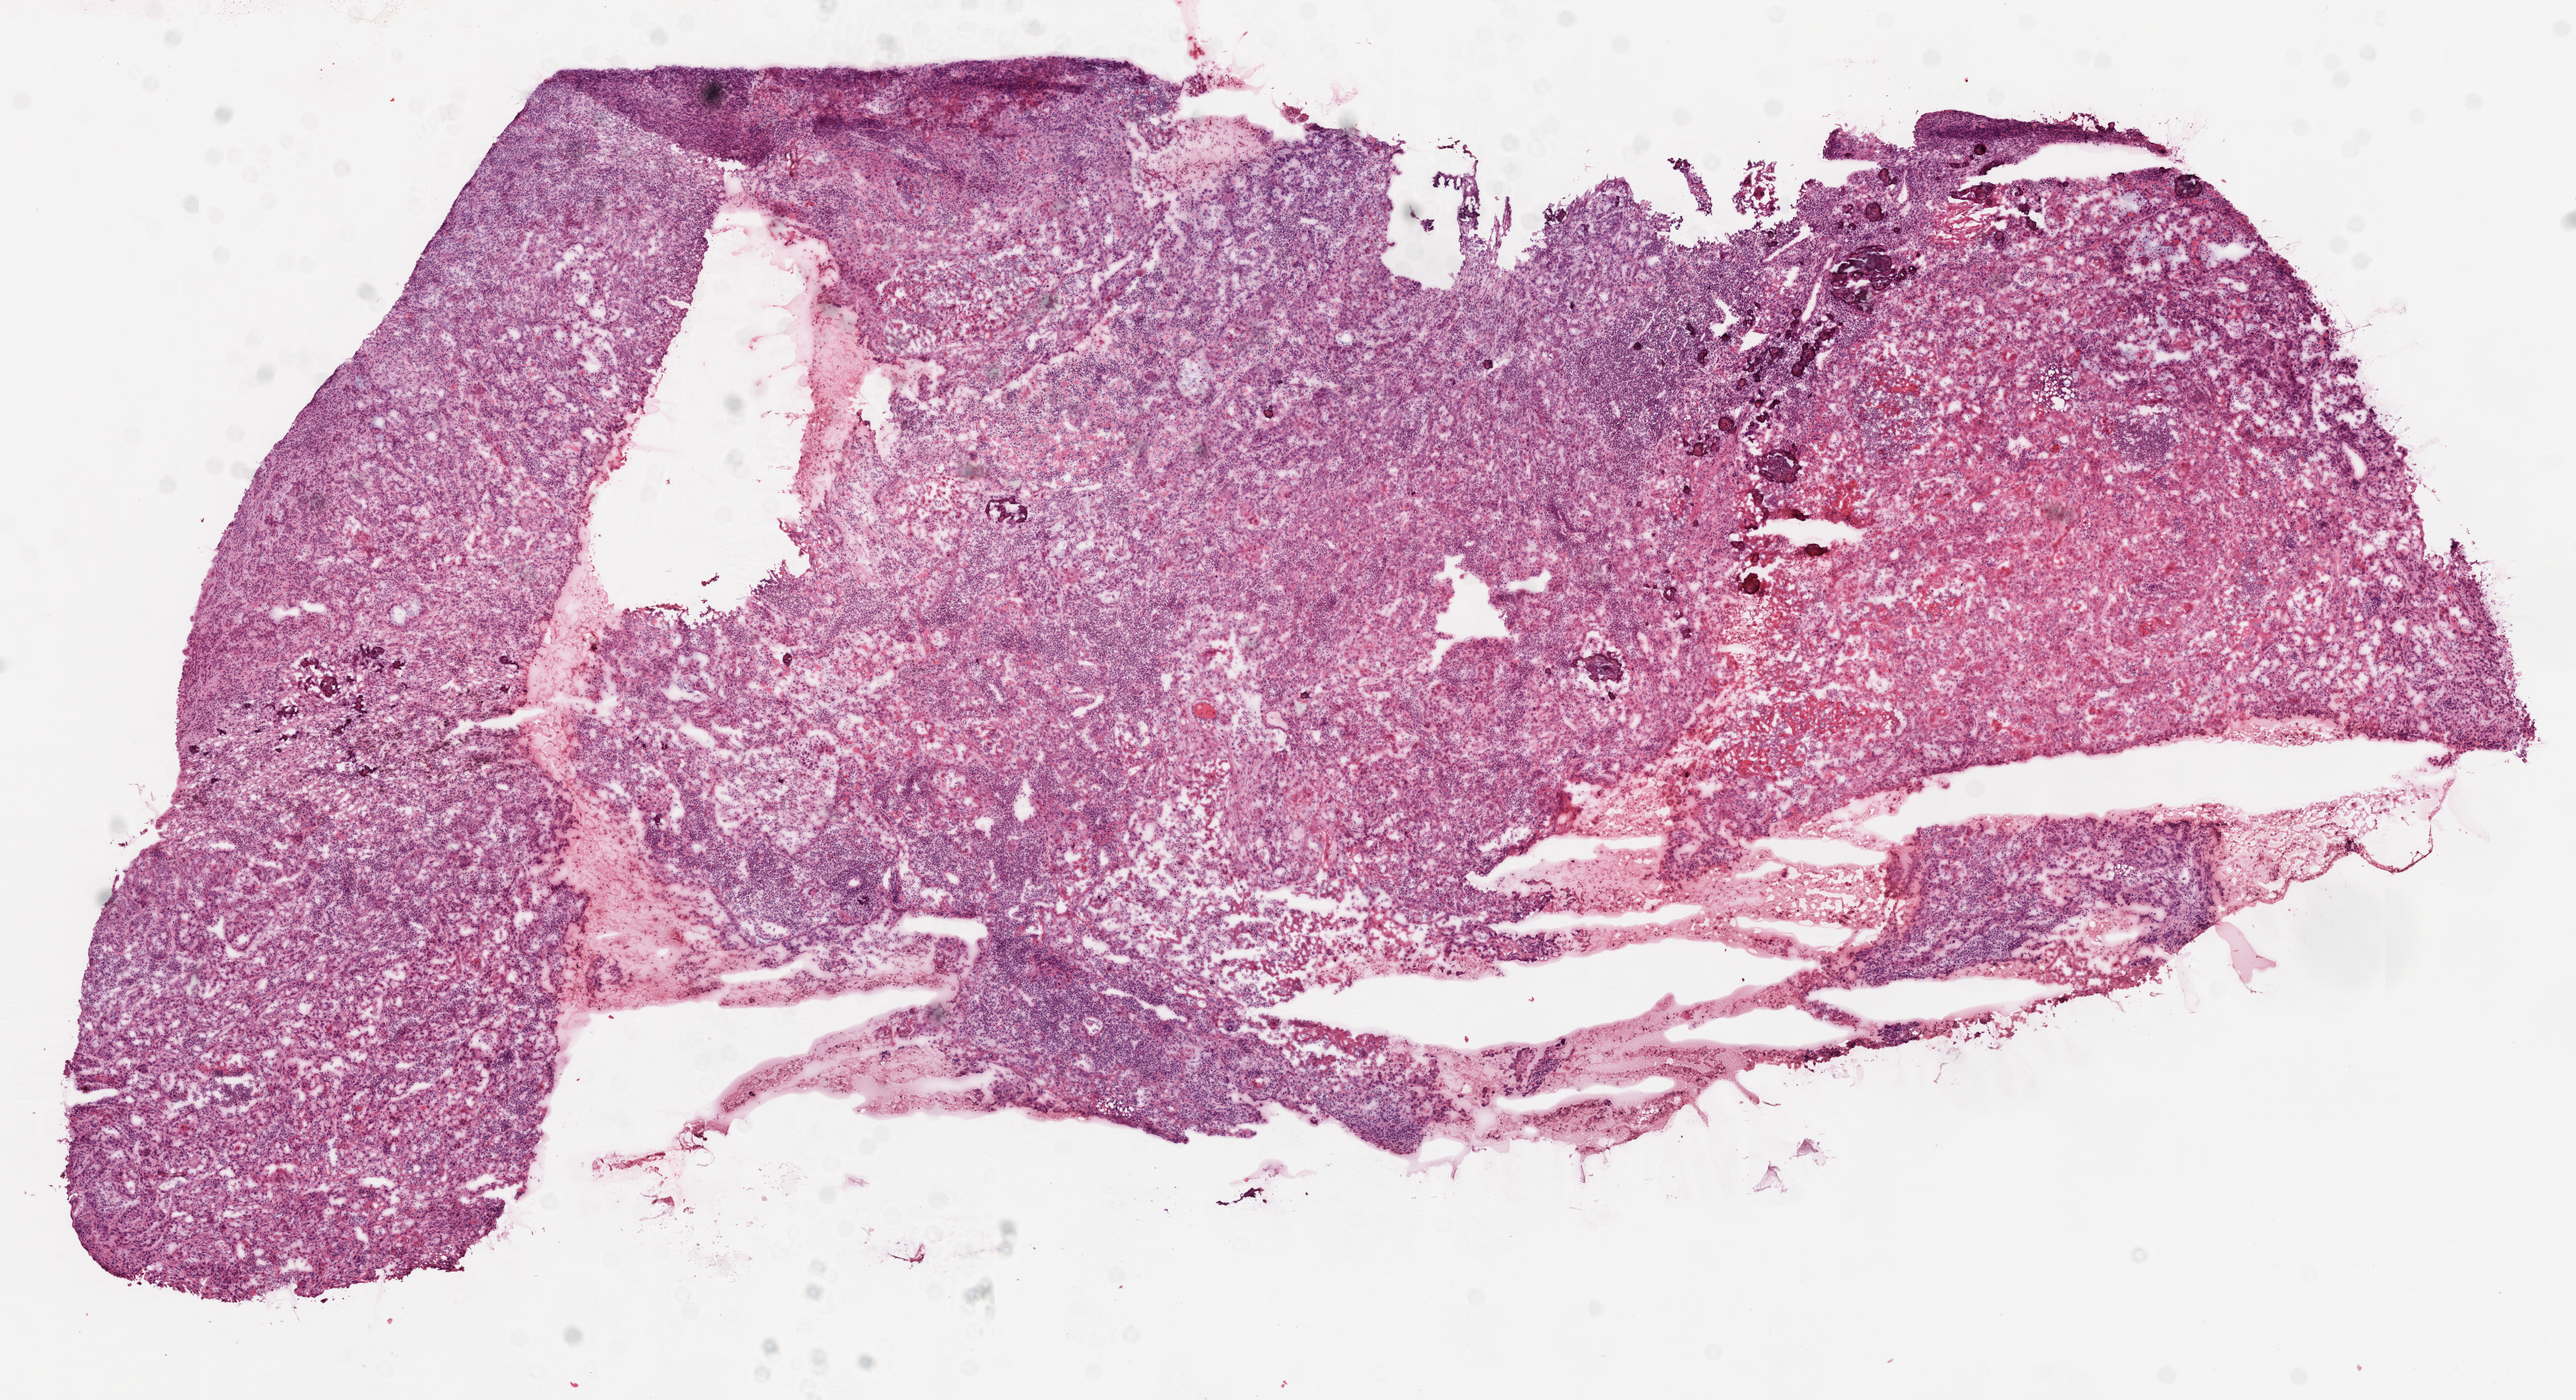
Digitized H&E tissue section (whole slide) — shown as a low-resolution overview of the whole scanned area (about 13.0 x 7.1 mm). Frozen section. Sample: primary tumour, lung. Female, age 62 years at initial diagnosis. Pathologist review of this section (percent, as recorded): tumour cells 85%, tumour nuclei 60%, normal cells 0%, stromal cells 10%, necrosis 5%.
AJCC pathologic stage: IIB (3rd edition). Pathologic diagnosis: Squamous cell carcinoma, NOS. Laterality: right.